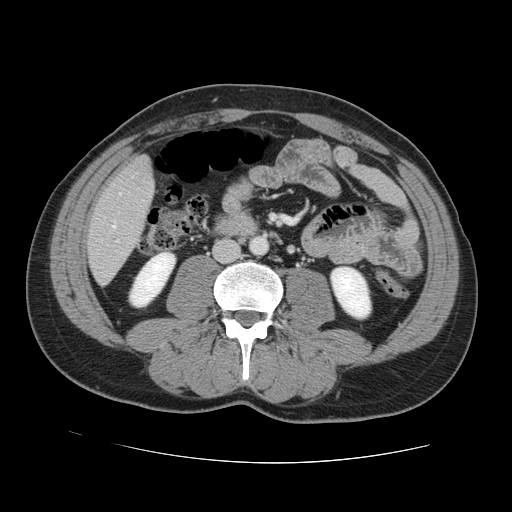
Contrast-enhanced abdominal CT, one axial slice. 120 kVp. Intravenous contrast given. Soft-tissue window (W 400 / L 40 HU). 2.5 mm slice thickness. 512 × 512 image matrix, field of view 380 × 380 mm. Male patient, age 40 years. From the clinical record (not read from this slice): diagnosis: colorectal cancer liver metastases, imaged before liver resection; multiple liver metastases: yes; largest metastasis: 2.9 cm; disease in both lobes: yes.
Outlined on this slice (outlined manually by an expert reader):
- hepatic veins: box from (x=112, y=193) to (x=121, y=228) px
- liver: (x=89, y=158)–(x=152, y=283)